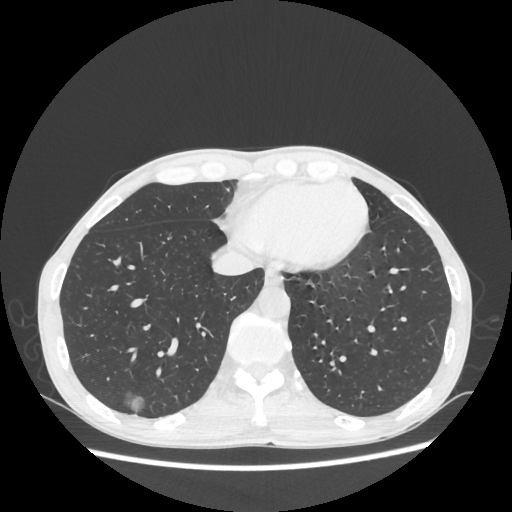
Chest CT, one axial slice. Slice 76 of 270 in the series (ordered by position). Reconstruction kernel STANDARD. 100 kVp. Lung window (W 1500 / L -600 HU). 1.25 mm slice thickness. 512 × 512 image matrix, field of view 360 × 360 mm. Patient: male, 60 years. Case-level facts recorded for this patient, not image findings: clinical TNM (as recorded): T1c N0 M0.
Annotated regions visible in this slice (bounding box drawn by a radiologist):
- lung tumour (recorded histology: adenocarcinoma): bounding box <119,389,152,415> (left, top, right, bottom; pixels)